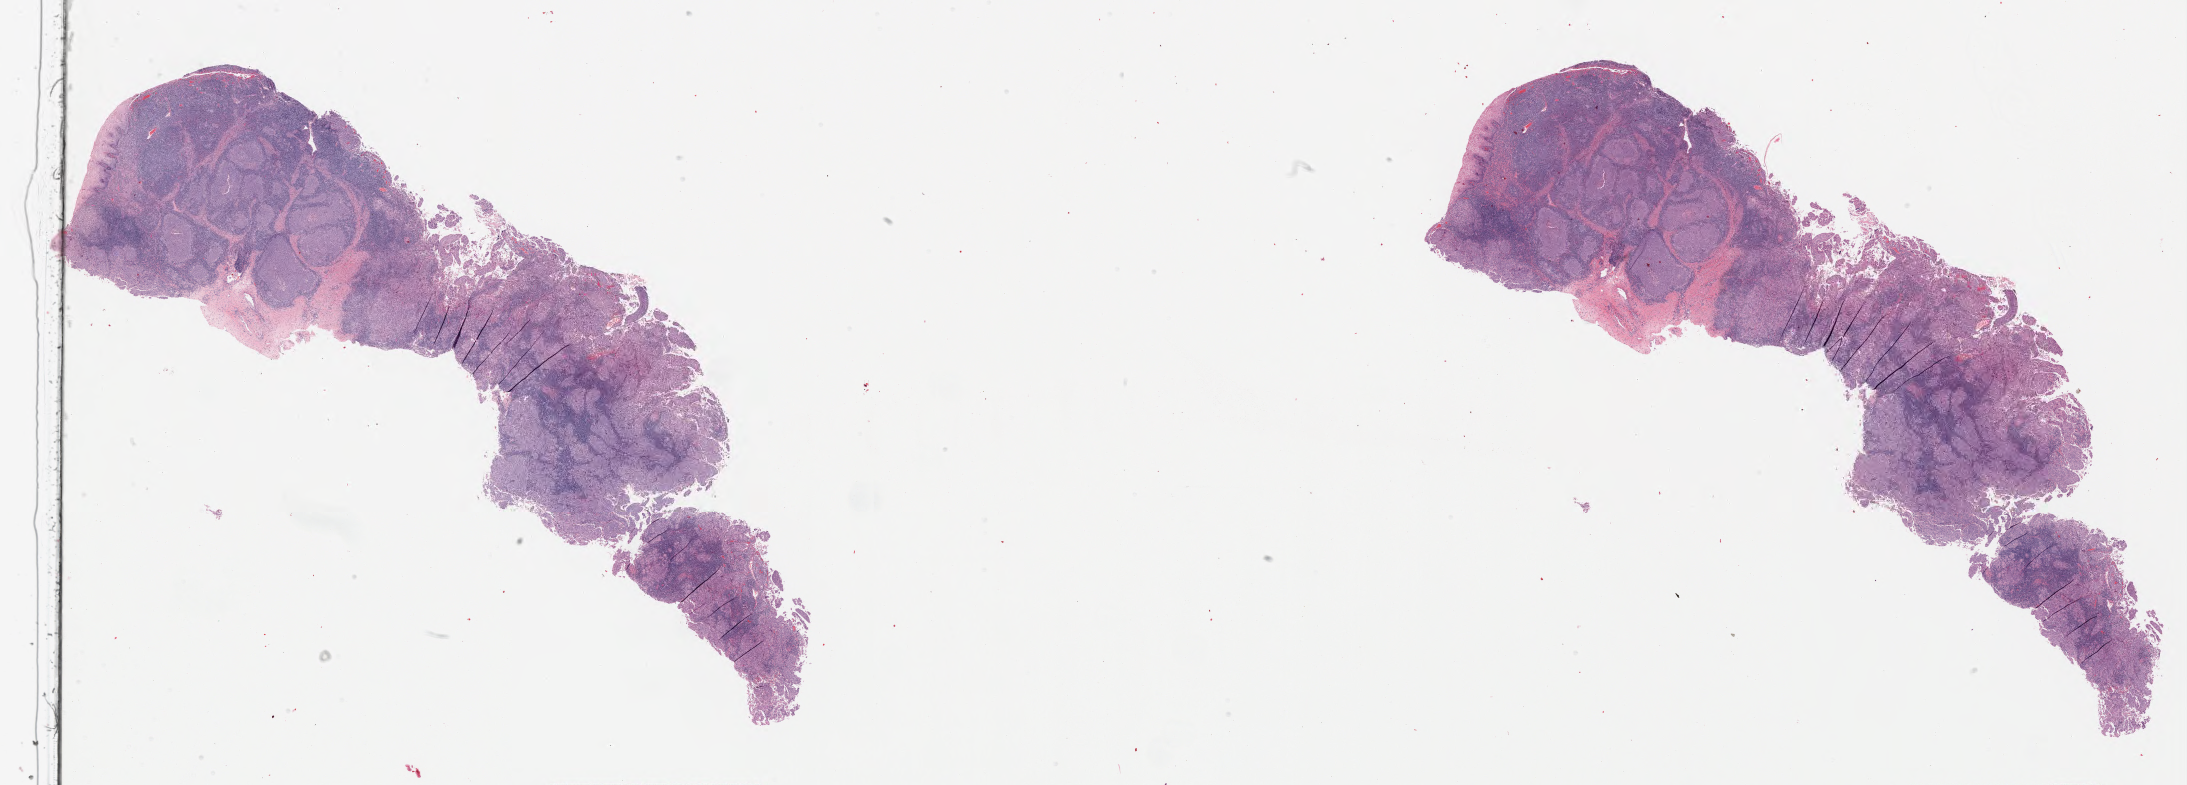
Whole-slide histology image, H&E-stained, low-resolution overview of the scanned area, about 35.0 x 12.6 mm (from a 20x scan); formalin-fixed paraffin-embedded (FFPE) diagnostic section; sample: primary tumour, cervix. Patient: female, age at initial diagnosis 46 years. Histologic grade: G2 (moderately differentiated).
Diagnosis: Squamous cell carcinoma, NOS (cervix uteri). FIGO stage: IB1.